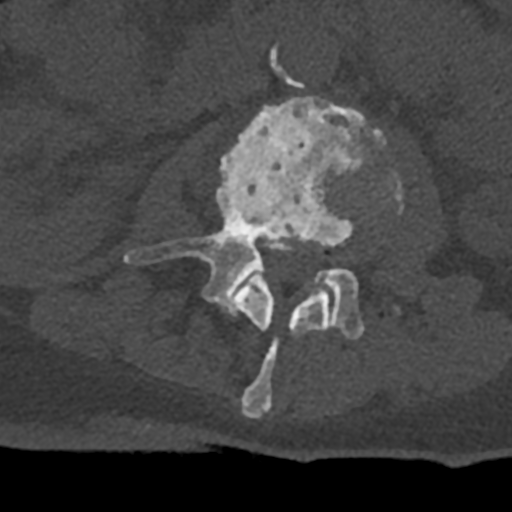
CT including the spine, one axial slice; position 344 of 797 along the scan axis; 120 kVp; bone window (W 1800 / L 400 HU); 0.5 mm slice thickness; 512 × 512 image matrix, field of view 160 × 160 mm. Patient: male, 74 years. From the clinical record (not read from this slice): primary cancer: renal; vertebrae with lytic lesions (as recorded): T10, L1, L2, L3, L4, L5.
Structures marked on this image (semi-automatically segmented with operator editing):
- L2 vertebra: box from (x=227, y=266) to (x=348, y=418) px
- L3 vertebra: (x=124, y=96)–(x=385, y=339)